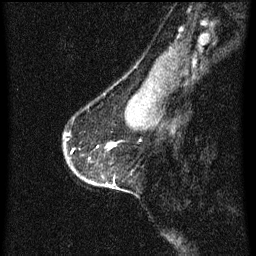
Breast MRI (dynamic contrast-enhanced), one sagittal slice; dynamic contrast-enhanced series, image 2 of 3 at this slice position (ordered by acquisition); 1.5 T; TE 4.2 ms, TR 8 ms; 256 × 256 image matrix, field of view 180 × 180 mm. Patient: female, 56 years.
Structures marked on this image (semi-automatic segmentation, software-assisted and operator-edited):
- analysis volume of interest (the breast-tissue region the enhancement analysis was run in; not a lesion): bounding box (x1, y1, x2, y2) in pixels: (64, 142, 120, 191)
- tumour enhancement mask (voxels above the 70 % enhancement threshold inside the analysis volume of interest): (107, 144, 114, 149)